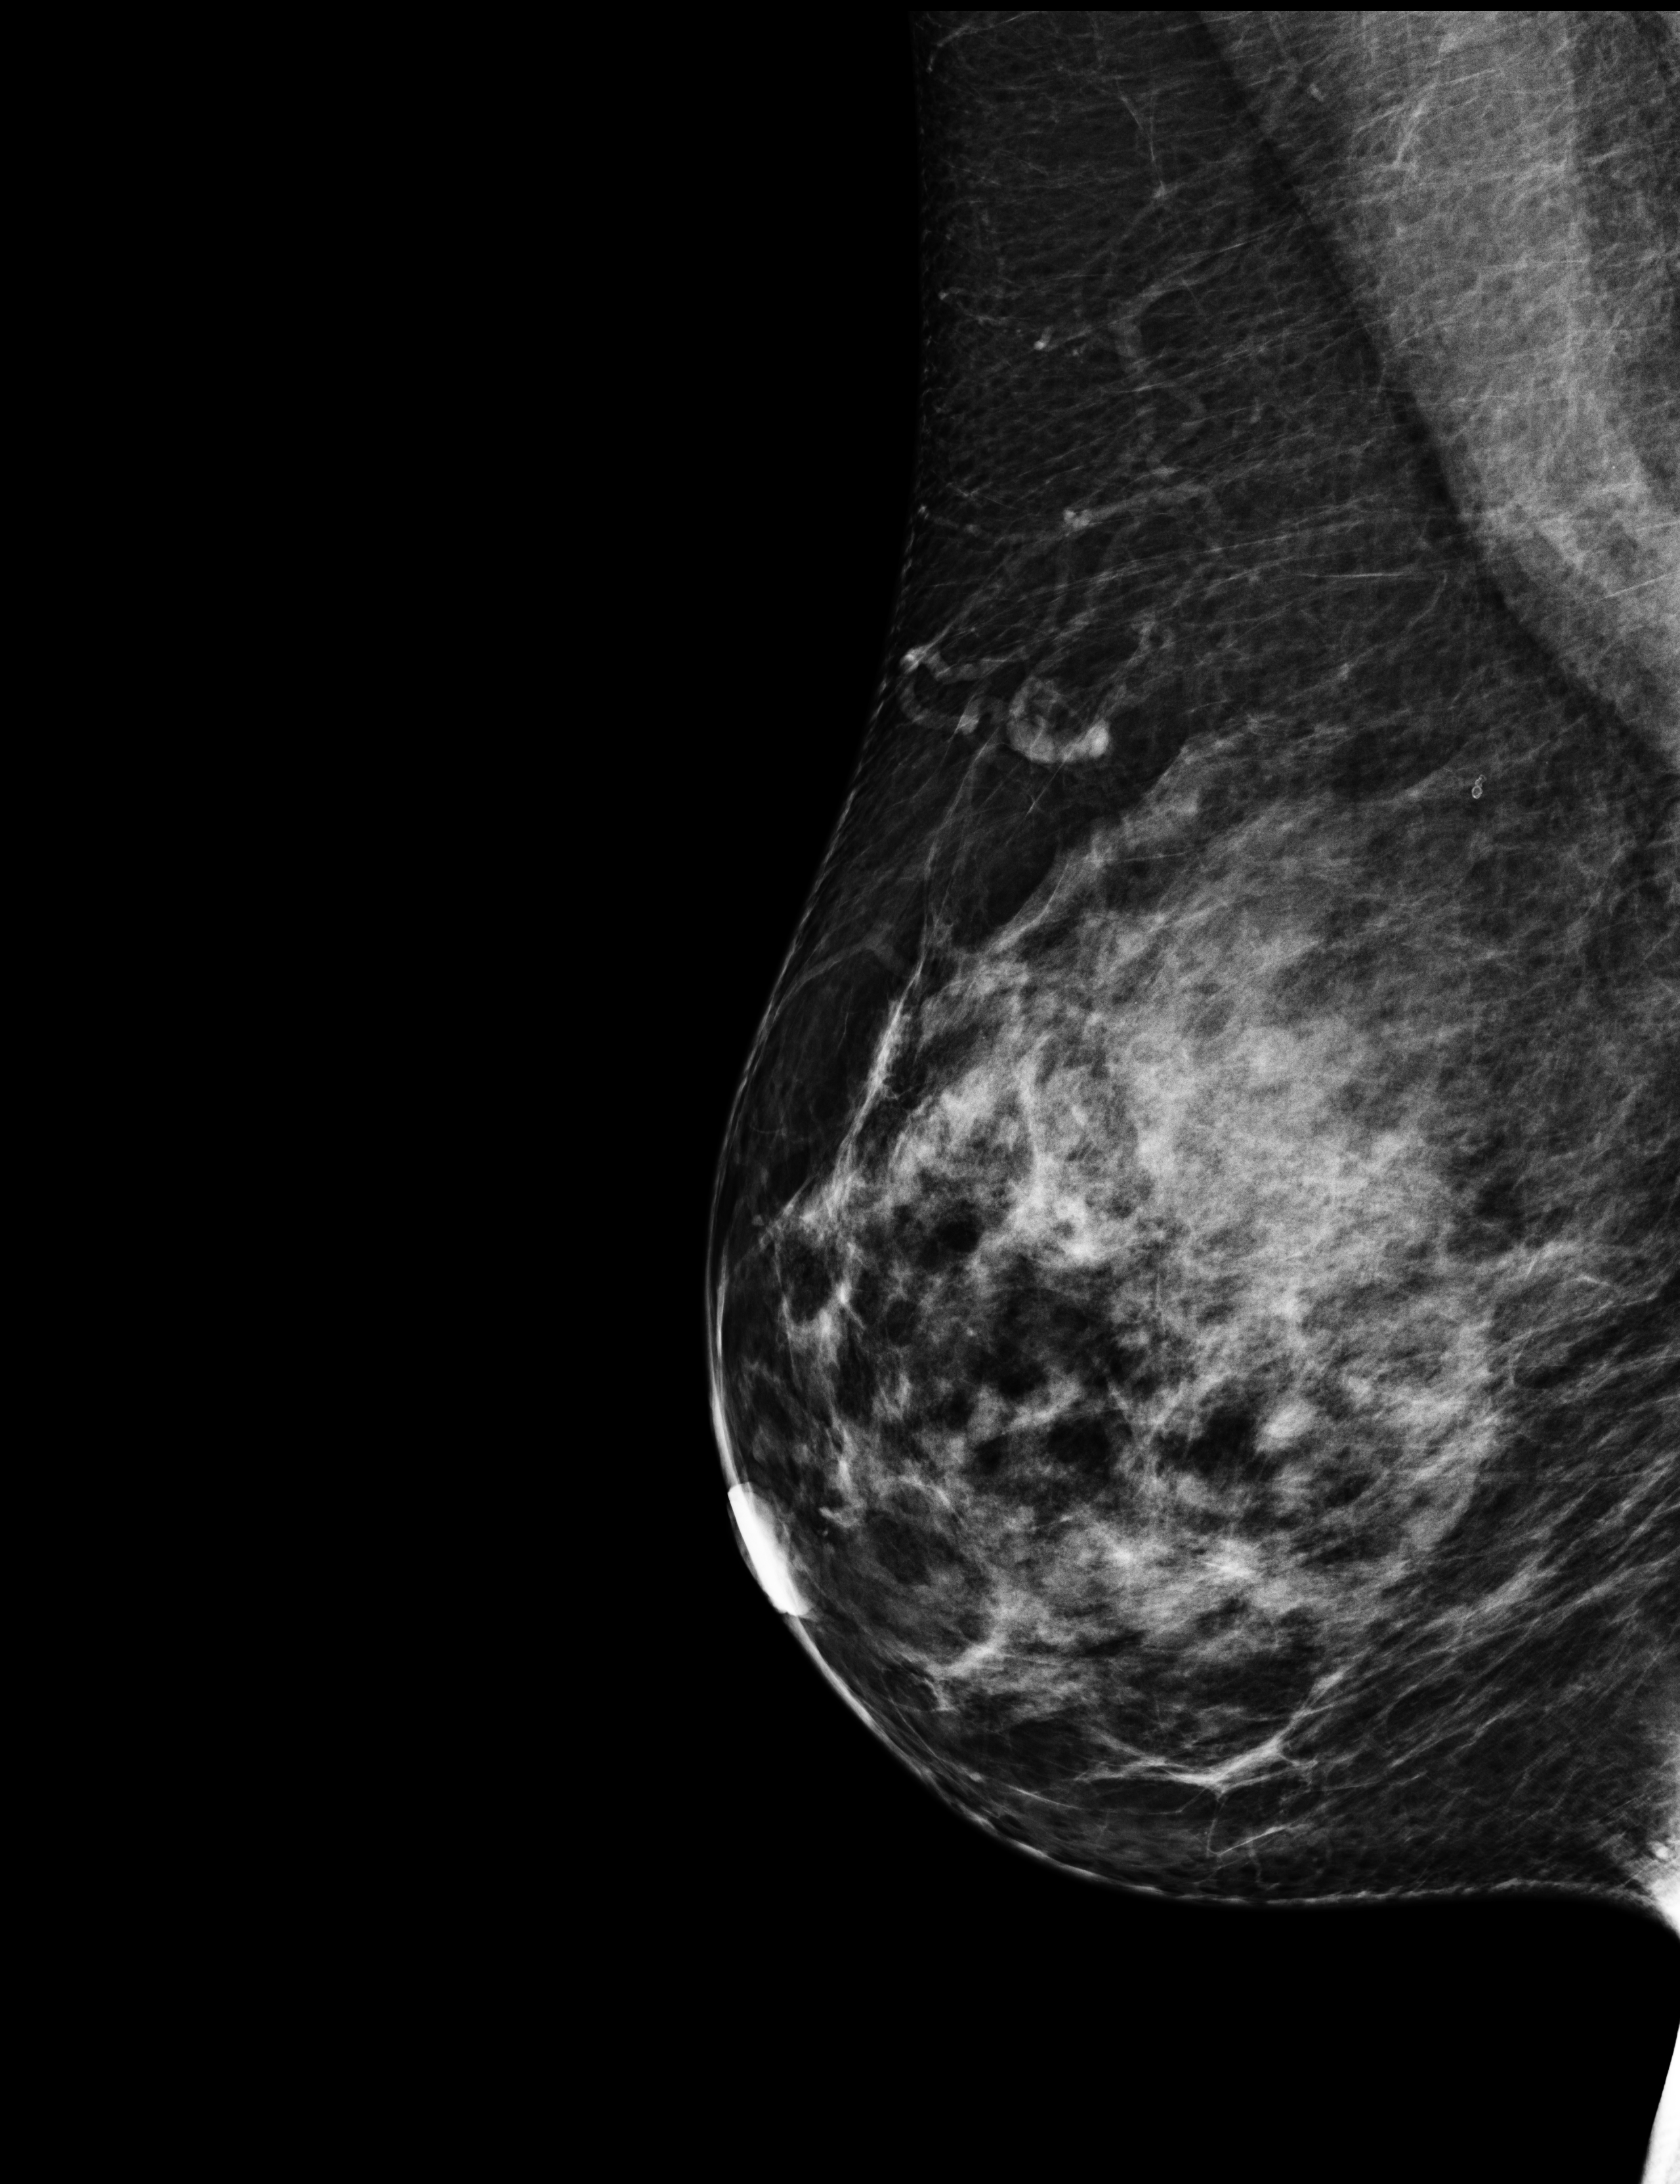
Annual screening mammography examination; compressed breast thickness 74 mm. Patient: female, 47 years.
Image type: full-field digital mammogram. Breast: right. Projection: MLO view.